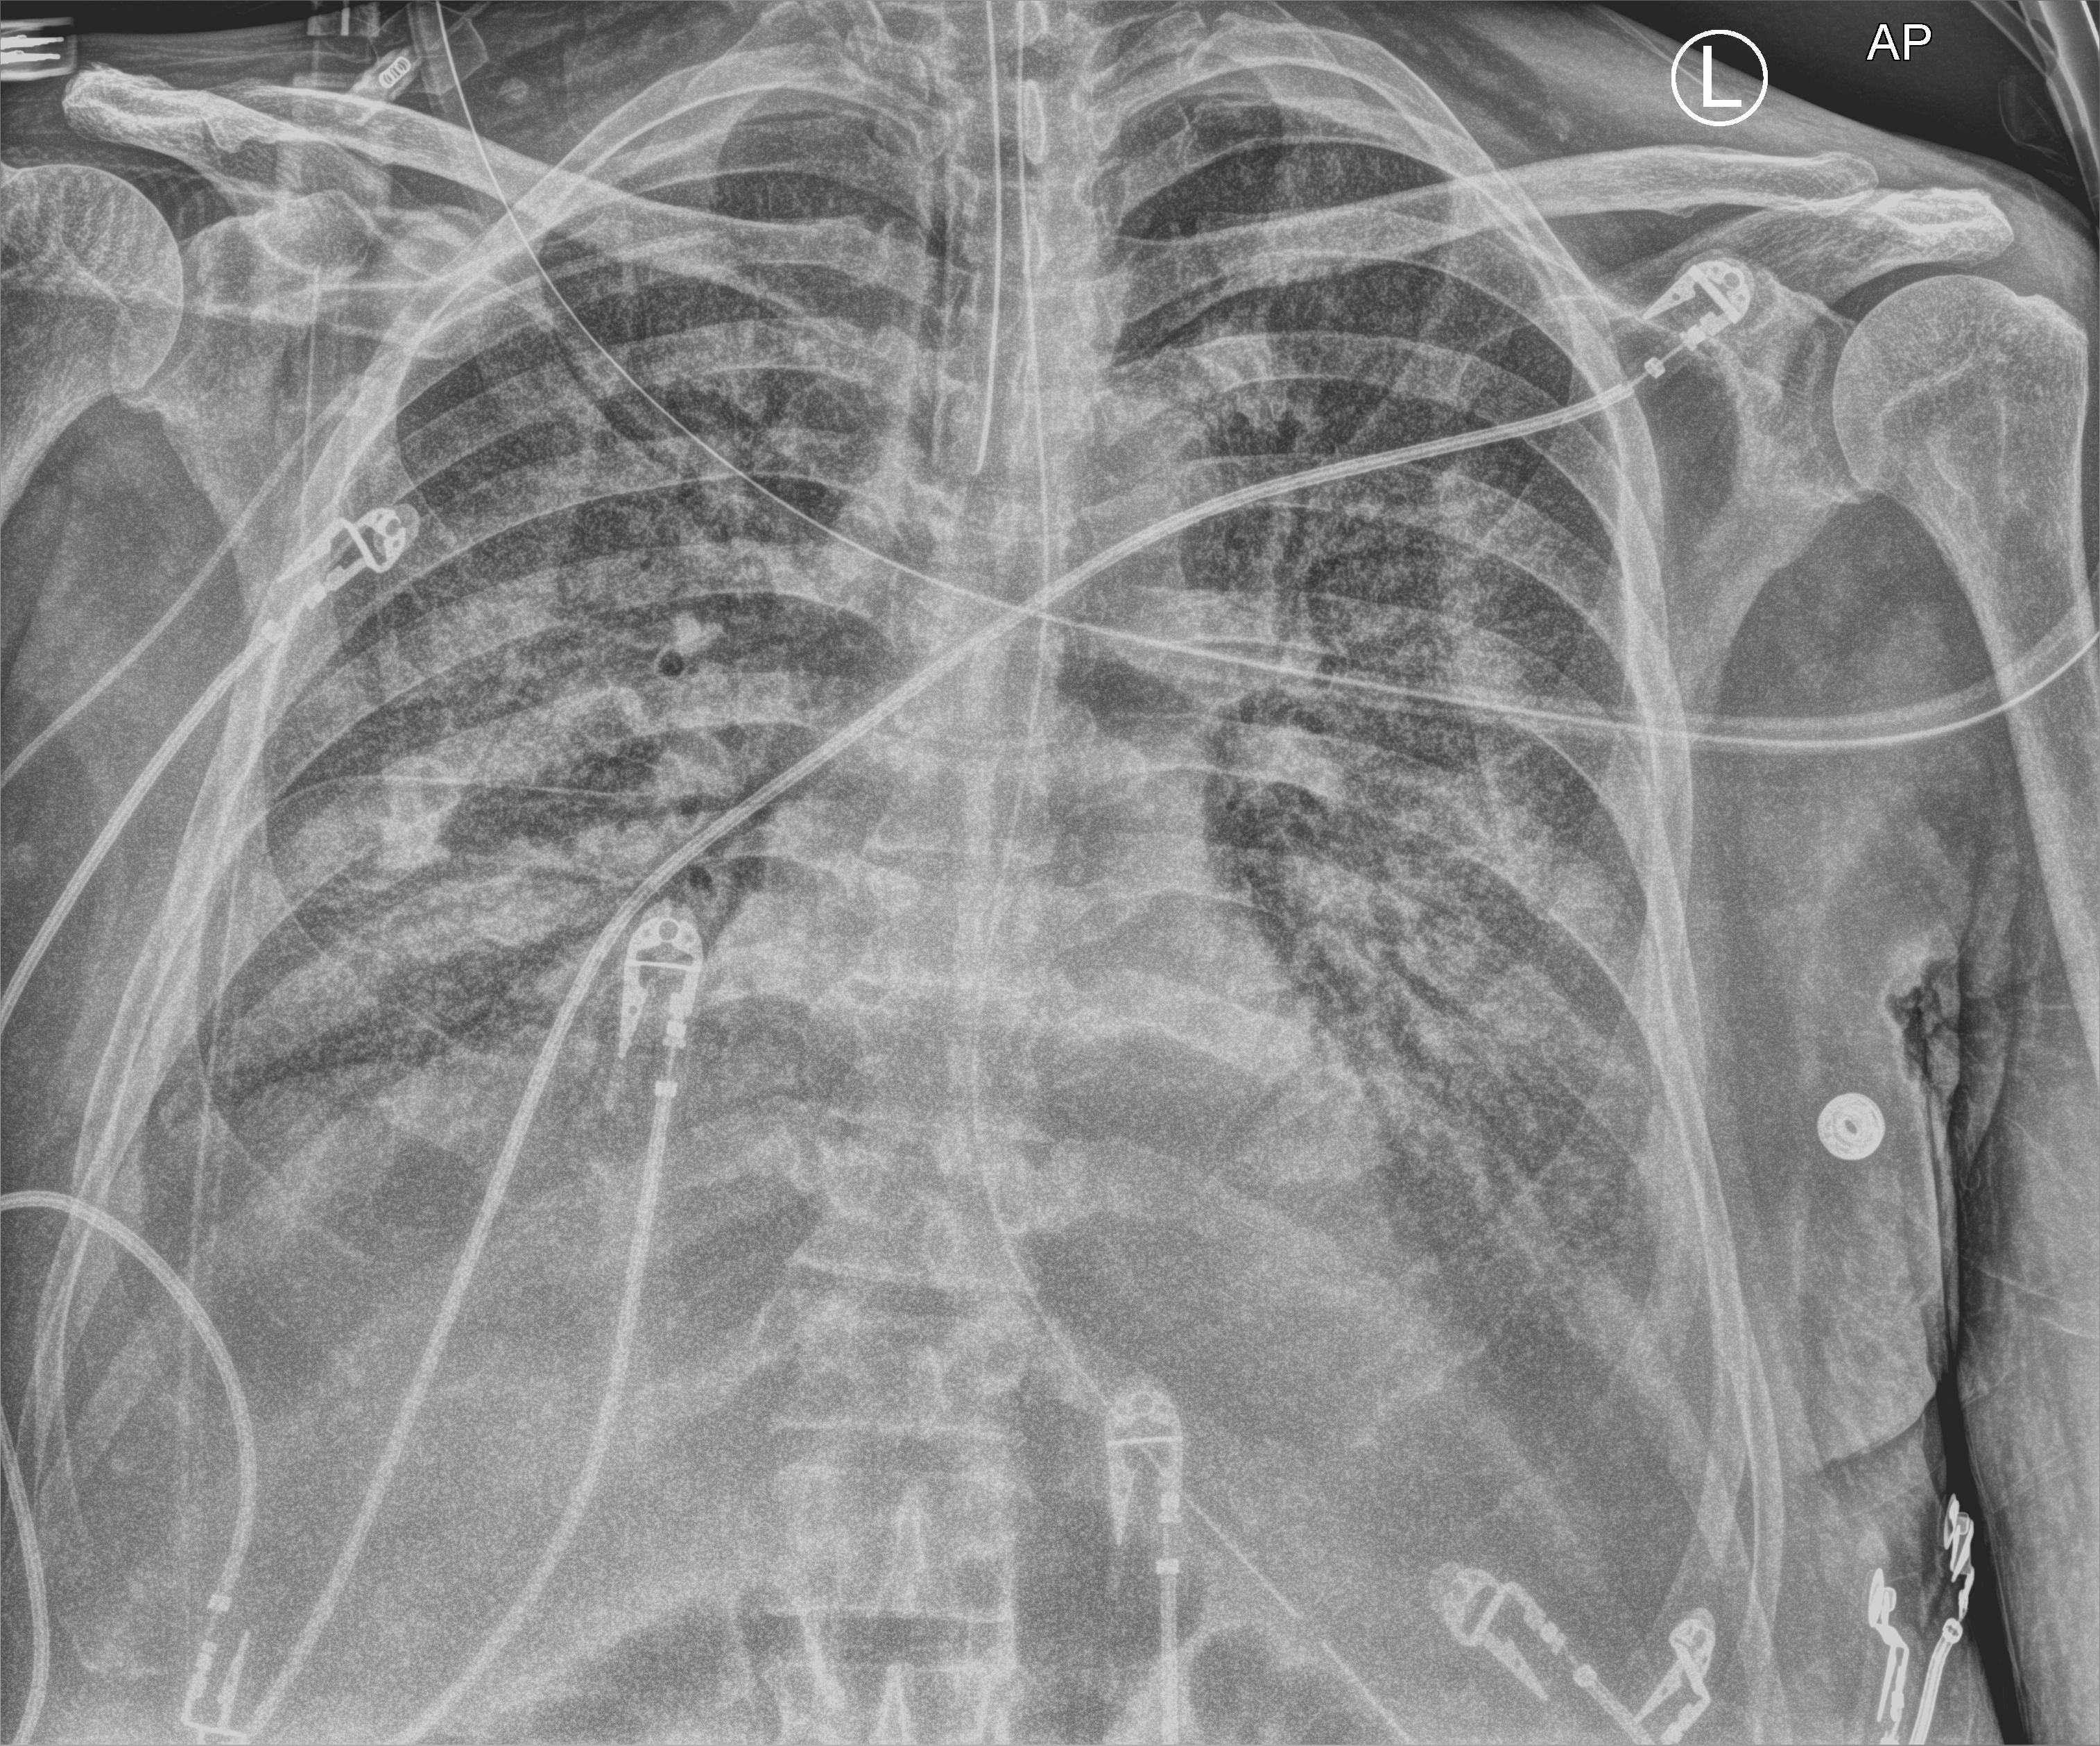
Bedside chest radiograph (computed radiography), anteroposterior (AP) projection. Patient hospitalised with COVID-19; male, aged 60–74 years.
From the hospital-stay record, not from the radiograph (when in the stay this image was taken is not recorded):
- length of hospital stay: 24 days